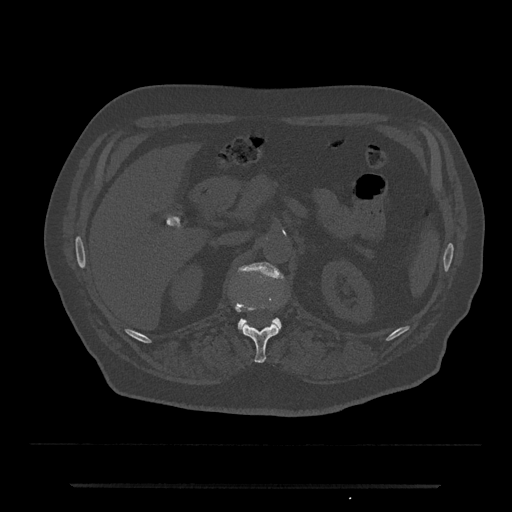
CT including the spine, one axial slice. Position 572 of 797 along the scan axis. Reconstruction kernel Br40s/3. Bone window (W 1800 / L 400 HU). 0.5 mm slice thickness. 512 × 512 image matrix, field of view 434 × 434 mm. Male patient, age 80 years. Case-level facts recorded for this patient, not image findings: primary cancer: prostate.
Annotated regions visible in this slice (semi-automatically segmented with operator editing):
- L1 vertebra: bounding box [x1, y1, x2, y2] px = [237, 262, 284, 331]
- T12 vertebra: [235, 302, 280, 363]